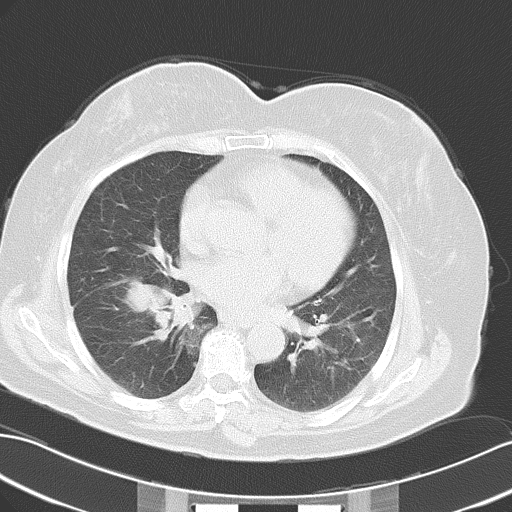
Chest CT, one axial slice. Position 25 of 50 along the scan axis. Reconstruction kernel B70f. Lung window (W 1500 / L -600 HU). 5 mm slice thickness. 512 × 512 image matrix, field of view 353 × 353 mm. Female patient, age 63 years. Case-level facts recorded for this patient, not image findings: clinical TNM (as recorded): T3 N0 M0.
Outlined on this slice (rectangle marked by the reading radiologist):
- lung tumour (recorded histology: adenocarcinoma): bounding box <120,276,195,340> (left, top, right, bottom; pixels)